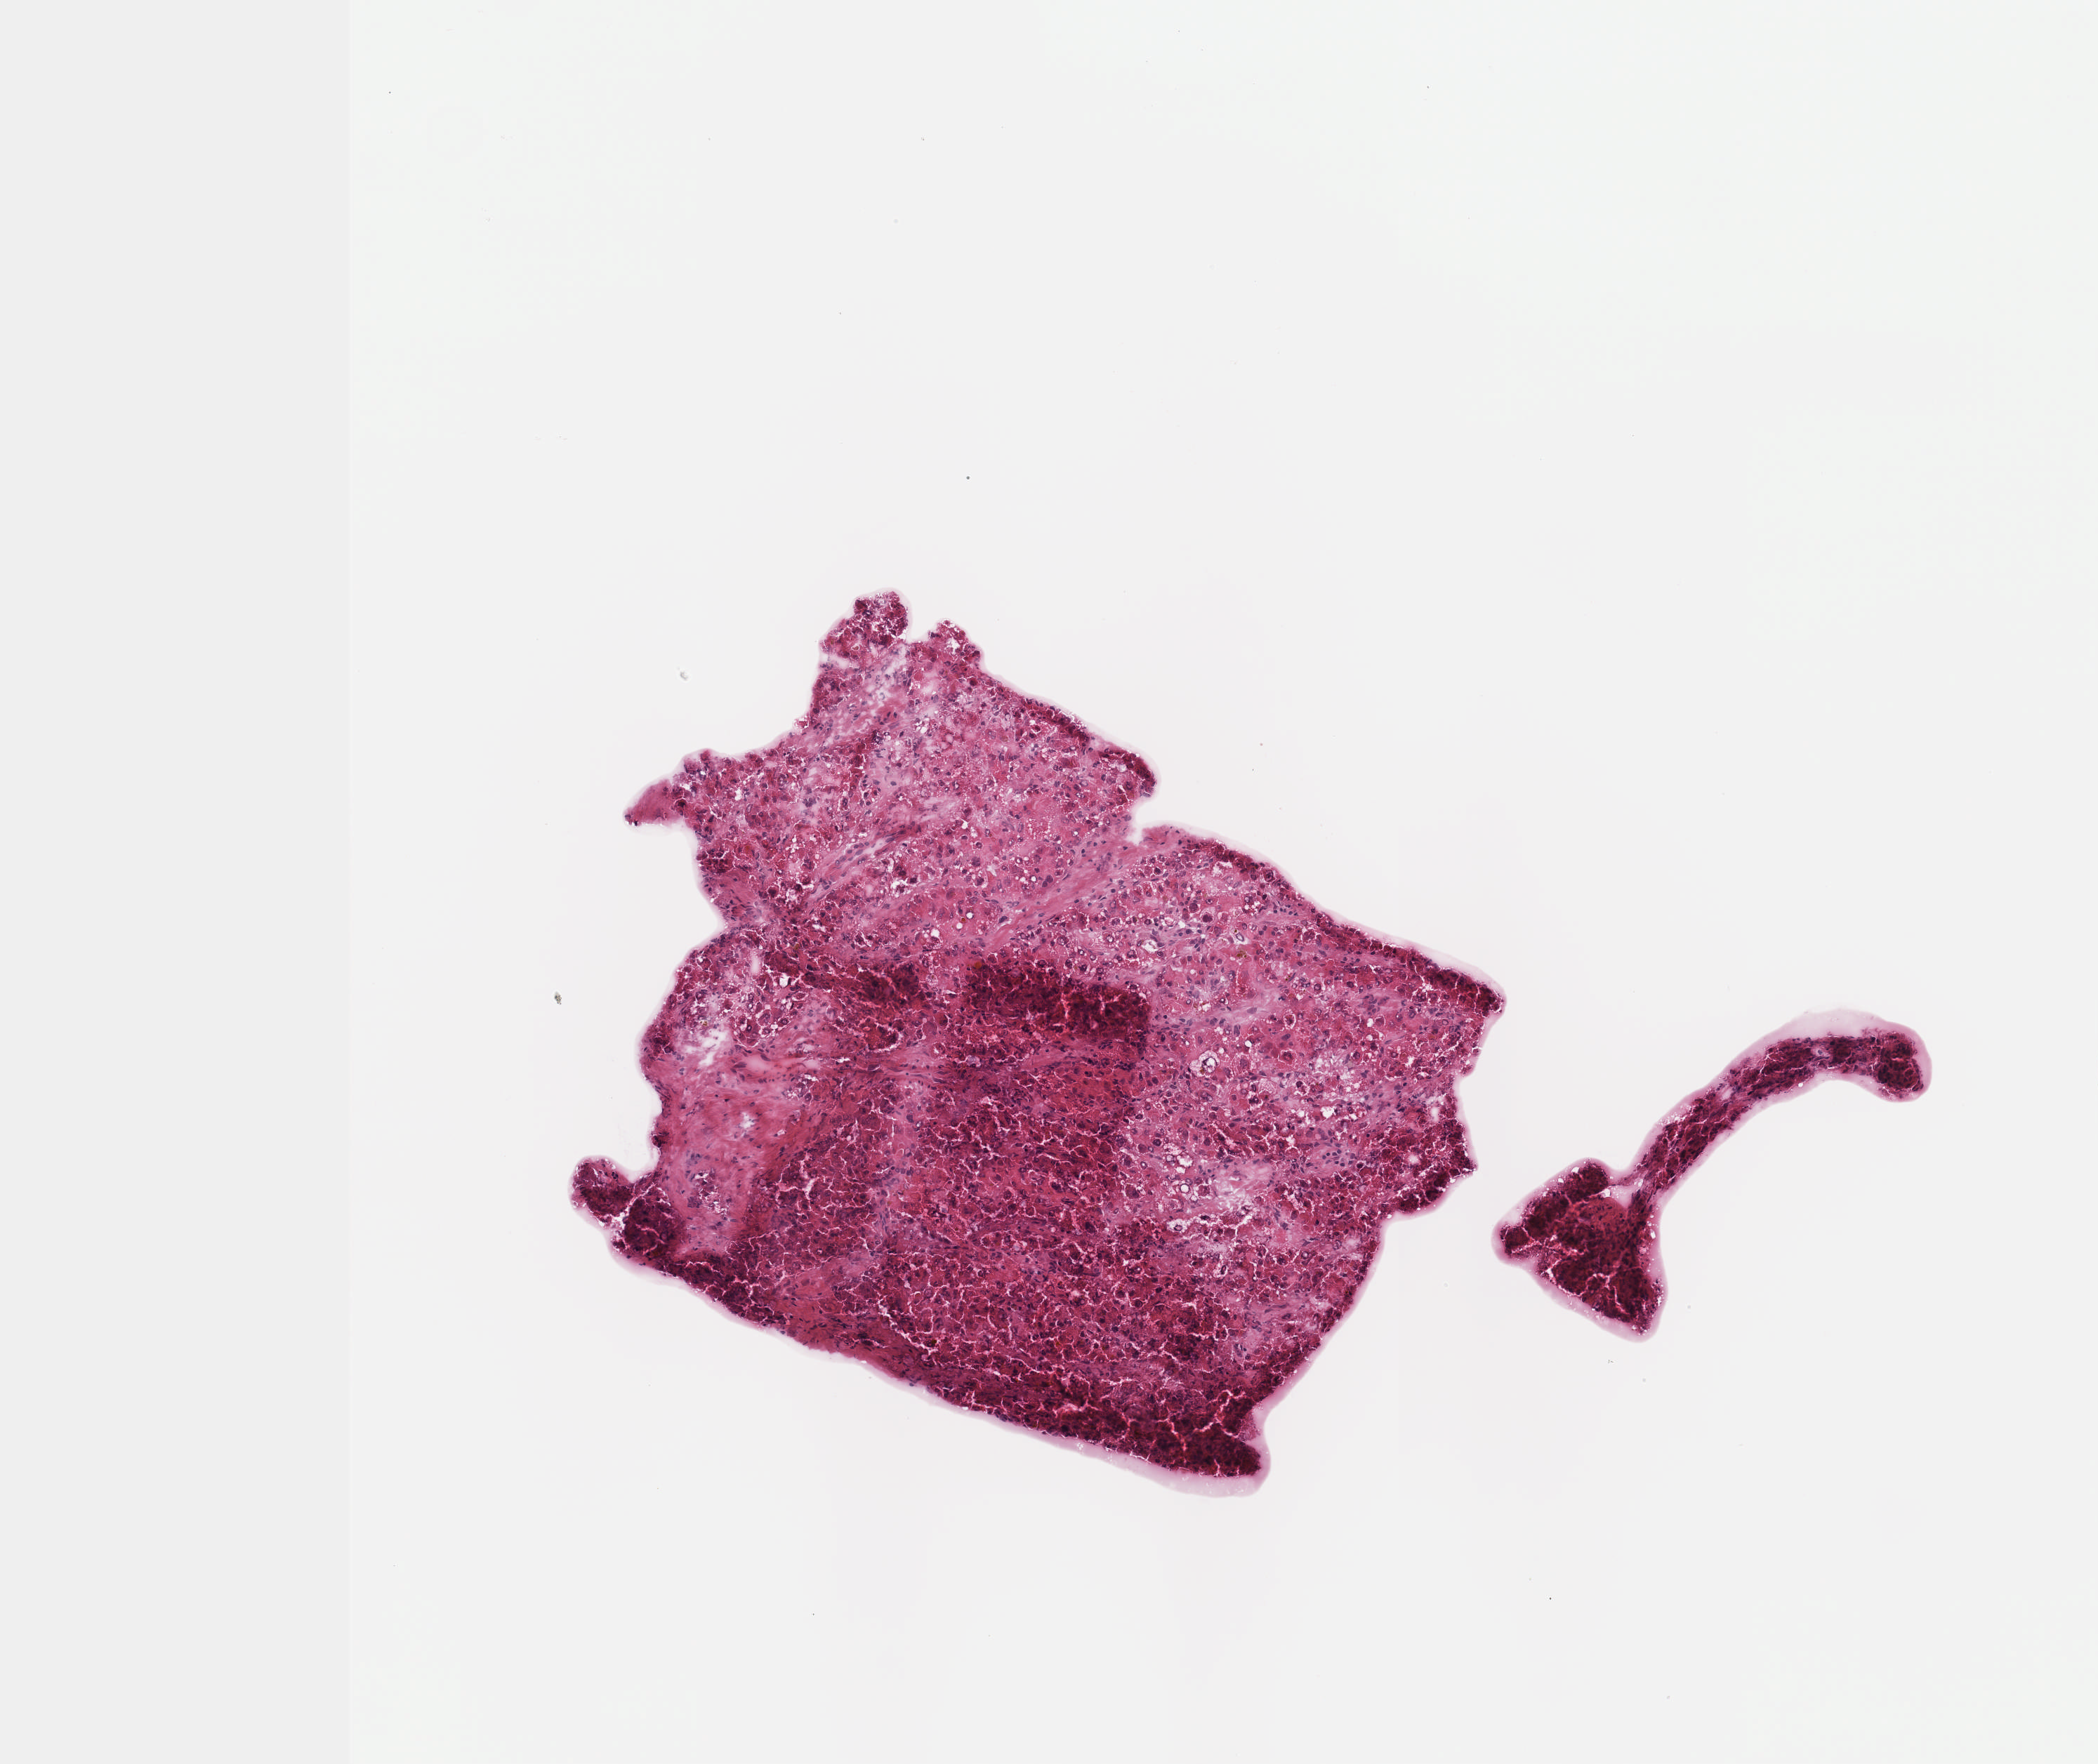
H&E-stained whole-slide image — shown as a low-resolution overview of the whole scanned area (about 3.0 x 2.5 mm, slide scanned at 40x). Frozen section. Liver, primary tumour sample. Patient: male, age at initial diagnosis 35 years. Histologic grade: G2 (moderately differentiated). Pathologist review of this section (percent, as recorded): tumour cells 80%, tumour nuclei 80%, normal cells 0%, stromal cells 20%, necrosis 0%. Inflammatory infiltration, as recorded: lymphocyte infiltration 3%, monocyte infiltration 1%, neutrophil infiltration 2%.
• histologic diagnosis: Hepatocellular carcinoma, NOS
• AJCC pathologic stage: I (6th edition)